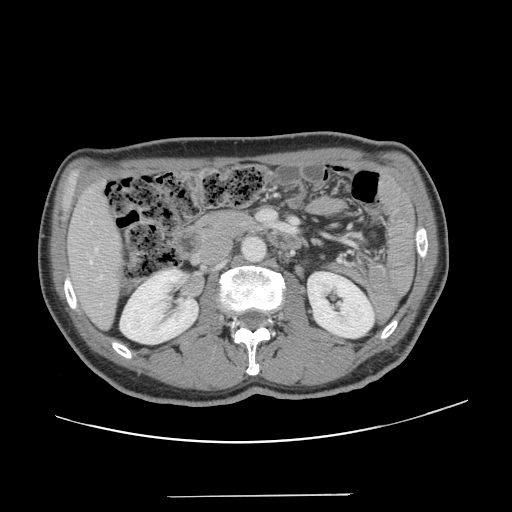
Contrast-enhanced abdominal CT, one axial slice; position 58 of 131 along the scan axis; 120 kVp; soft-tissue window (W 400 / L 40 HU); 512 × 512 image matrix, field of view 403 × 403 mm. Male patient, age 60 years. Case-level facts recorded for this patient, not image findings: diagnosis: colorectal cancer liver metastases, imaged before liver resection; multiple liver metastases: no; largest metastasis: 2.5 cm; disease in both lobes: no.
Annotated regions visible in this slice (expert manual segmentation):
- hepatic veins: bounding box <90,249,98,264> (left, top, right, bottom; pixels)
- liver: <69,186,121,327>
- planned liver remnant (the part of the liver to remain after resection): <69,186,121,327>